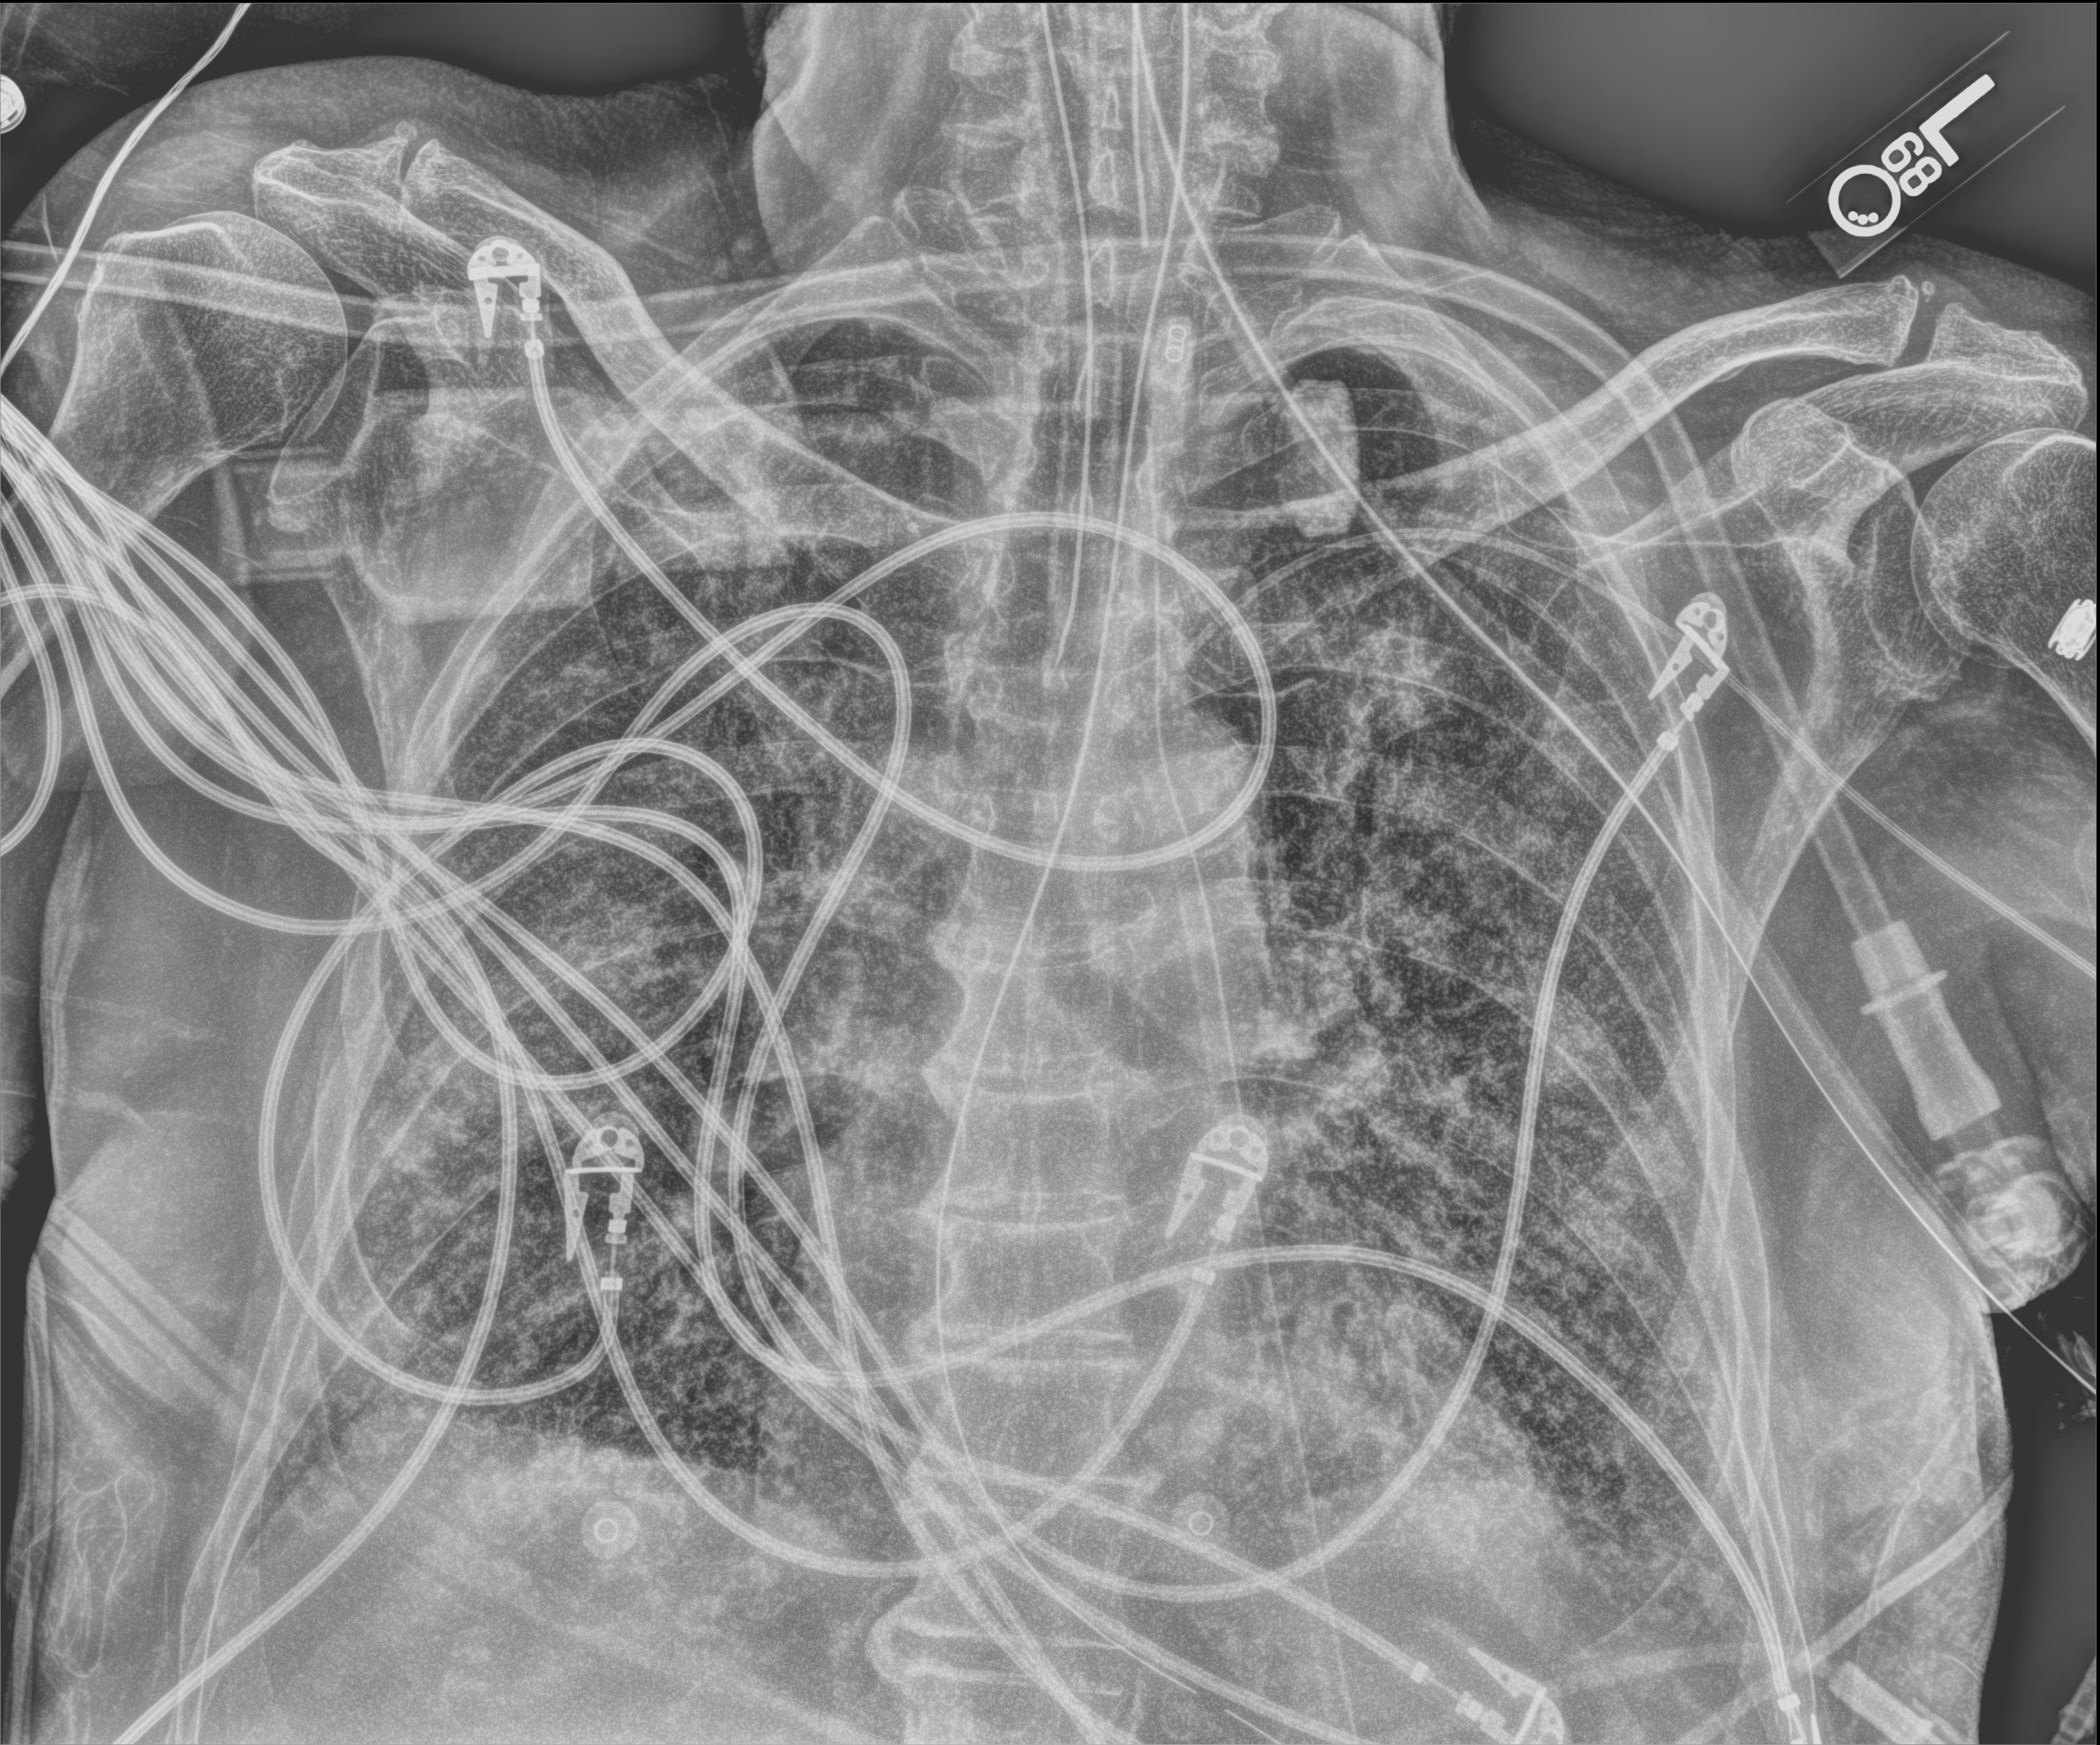
Chest X-ray (portable); anteroposterior (AP) projection. Male patient hospitalised with COVID-19, age 75–90 years.
Hospital-stay facts (about this admission, not read from this image; timing relative to this image not recorded):
- mechanically ventilated during this hospital stay: yes